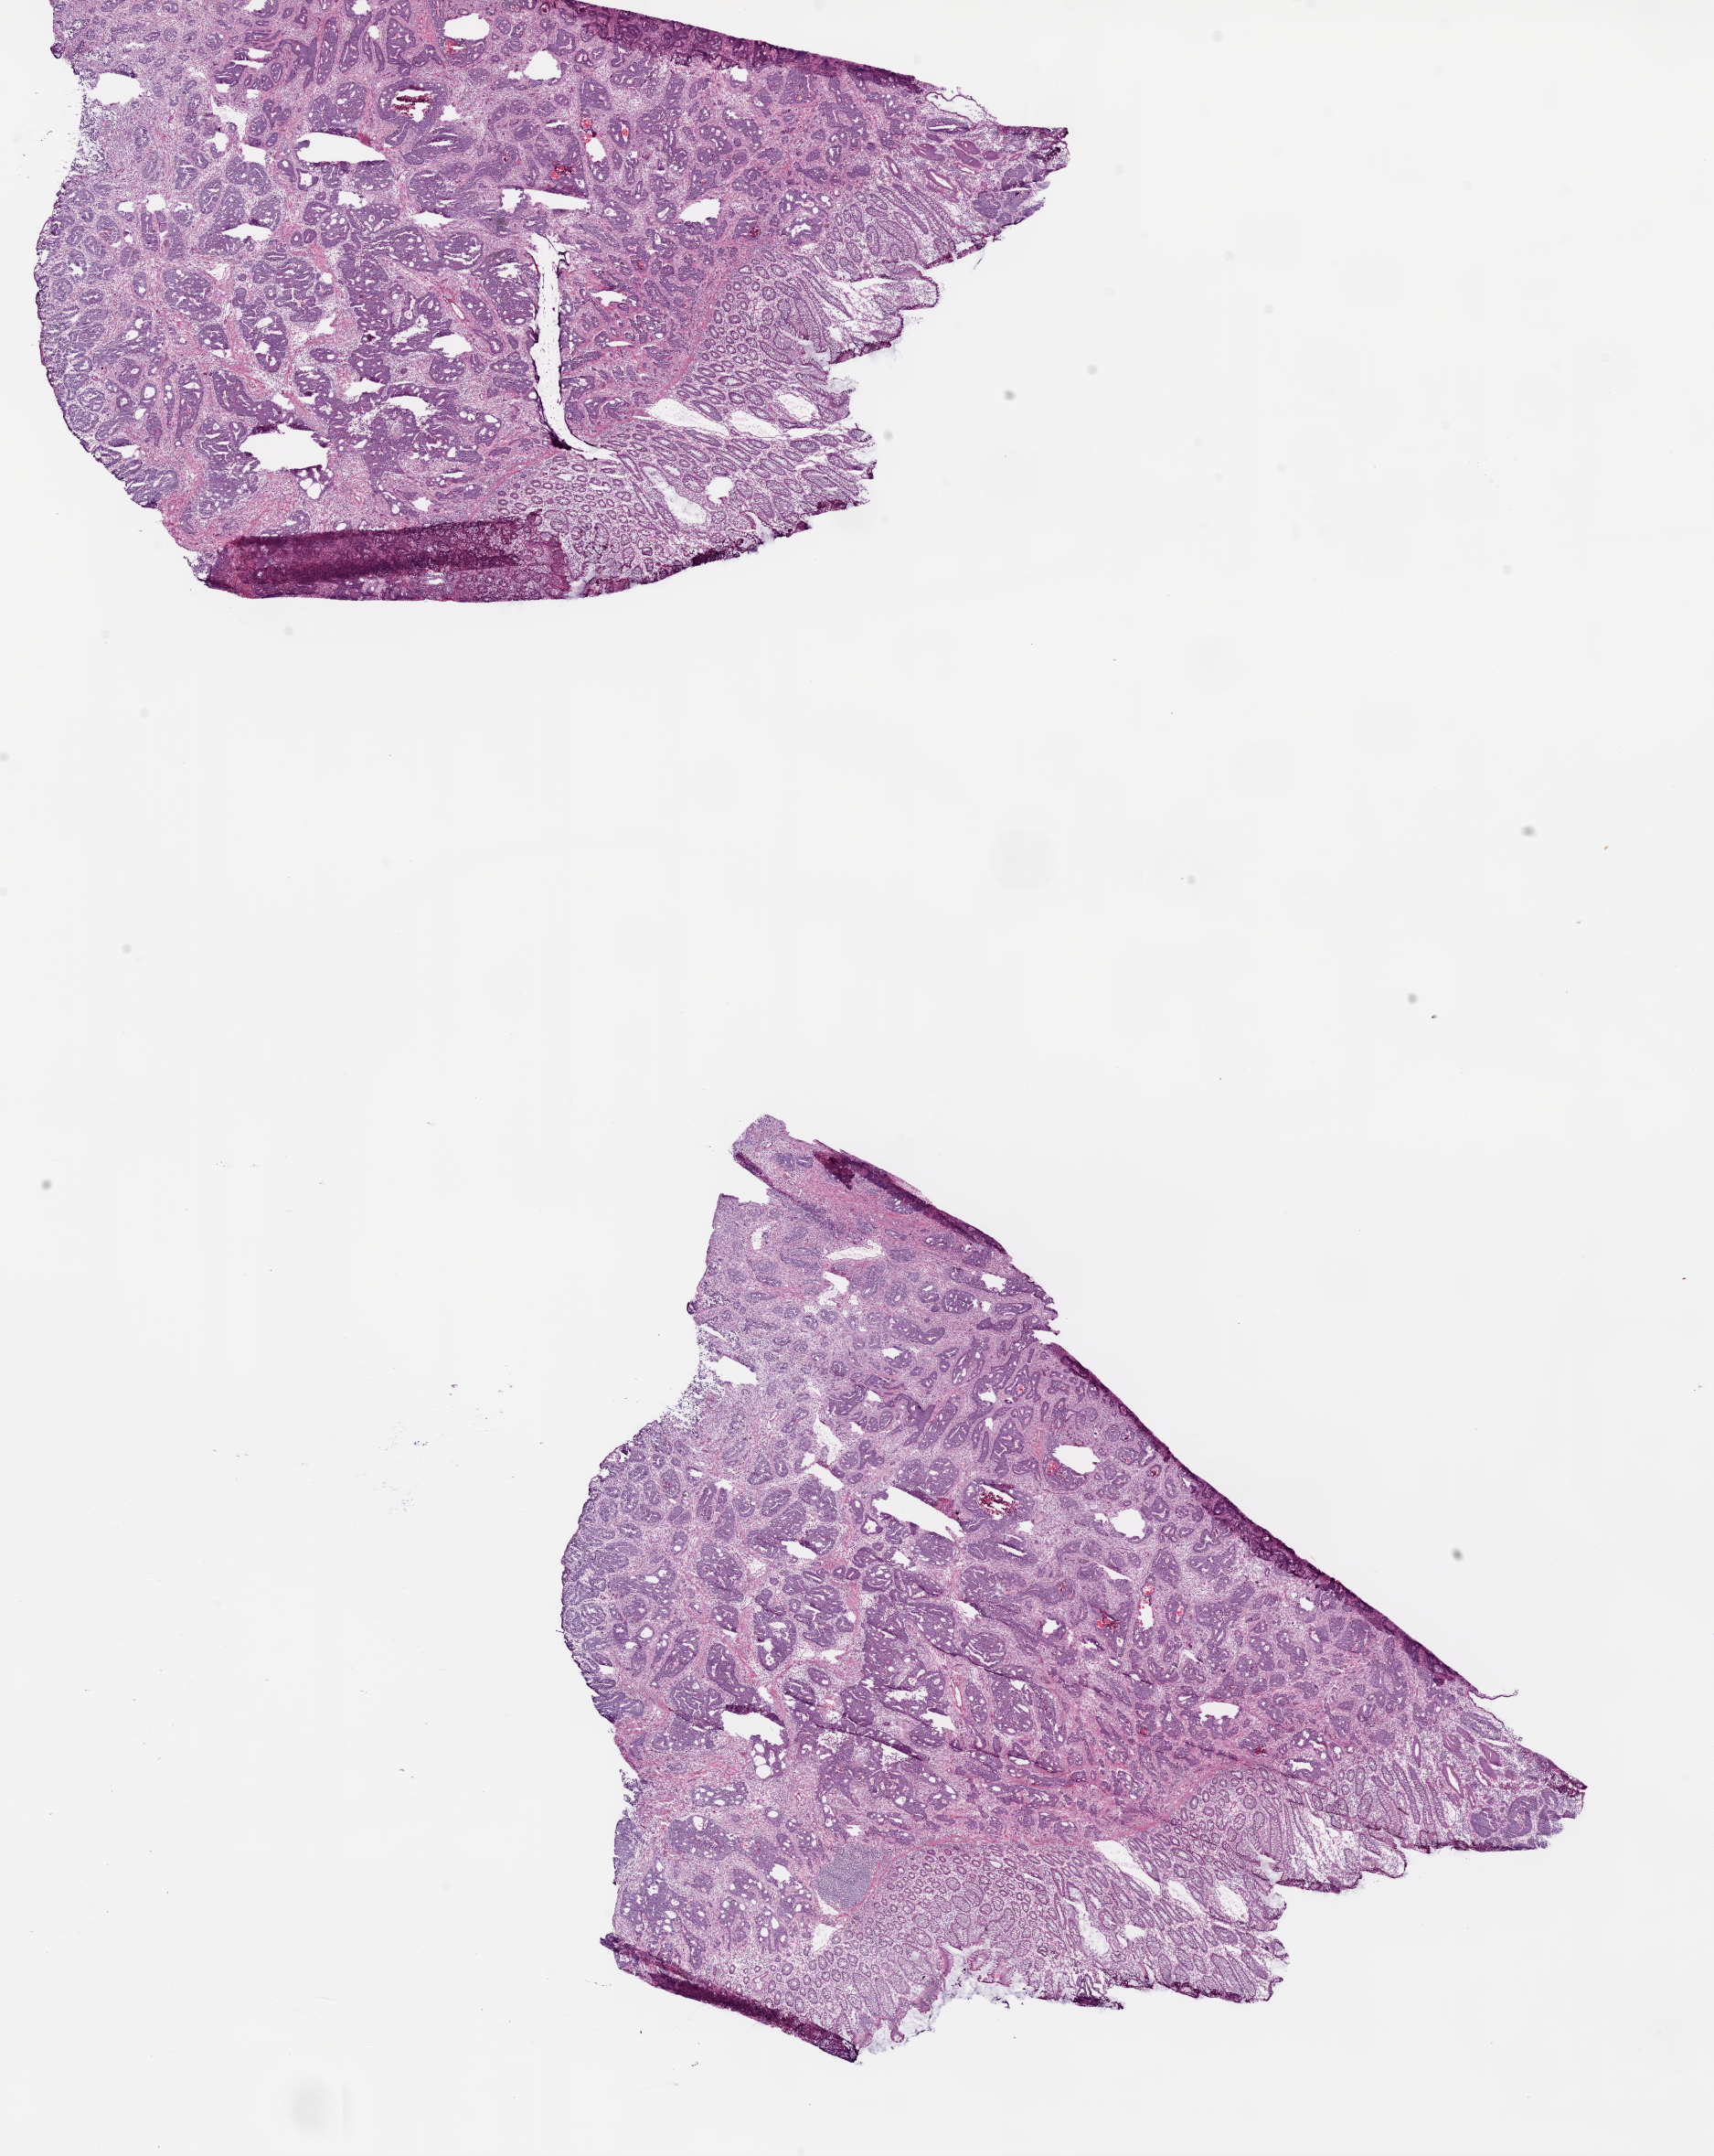
Whole-slide histology image, H&E, low-resolution overview of the scanned area, about 15.0 x 18.9 mm (slide scanned at 20x), frozen section, primary tumour sample from the colon. Patient: male, age at initial diagnosis 82 years. Pathologist review of this section (percent, as recorded): tumour cells 60%, tumour nuclei 70%.
Diagnosis: Adenocarcinoma, NOS.